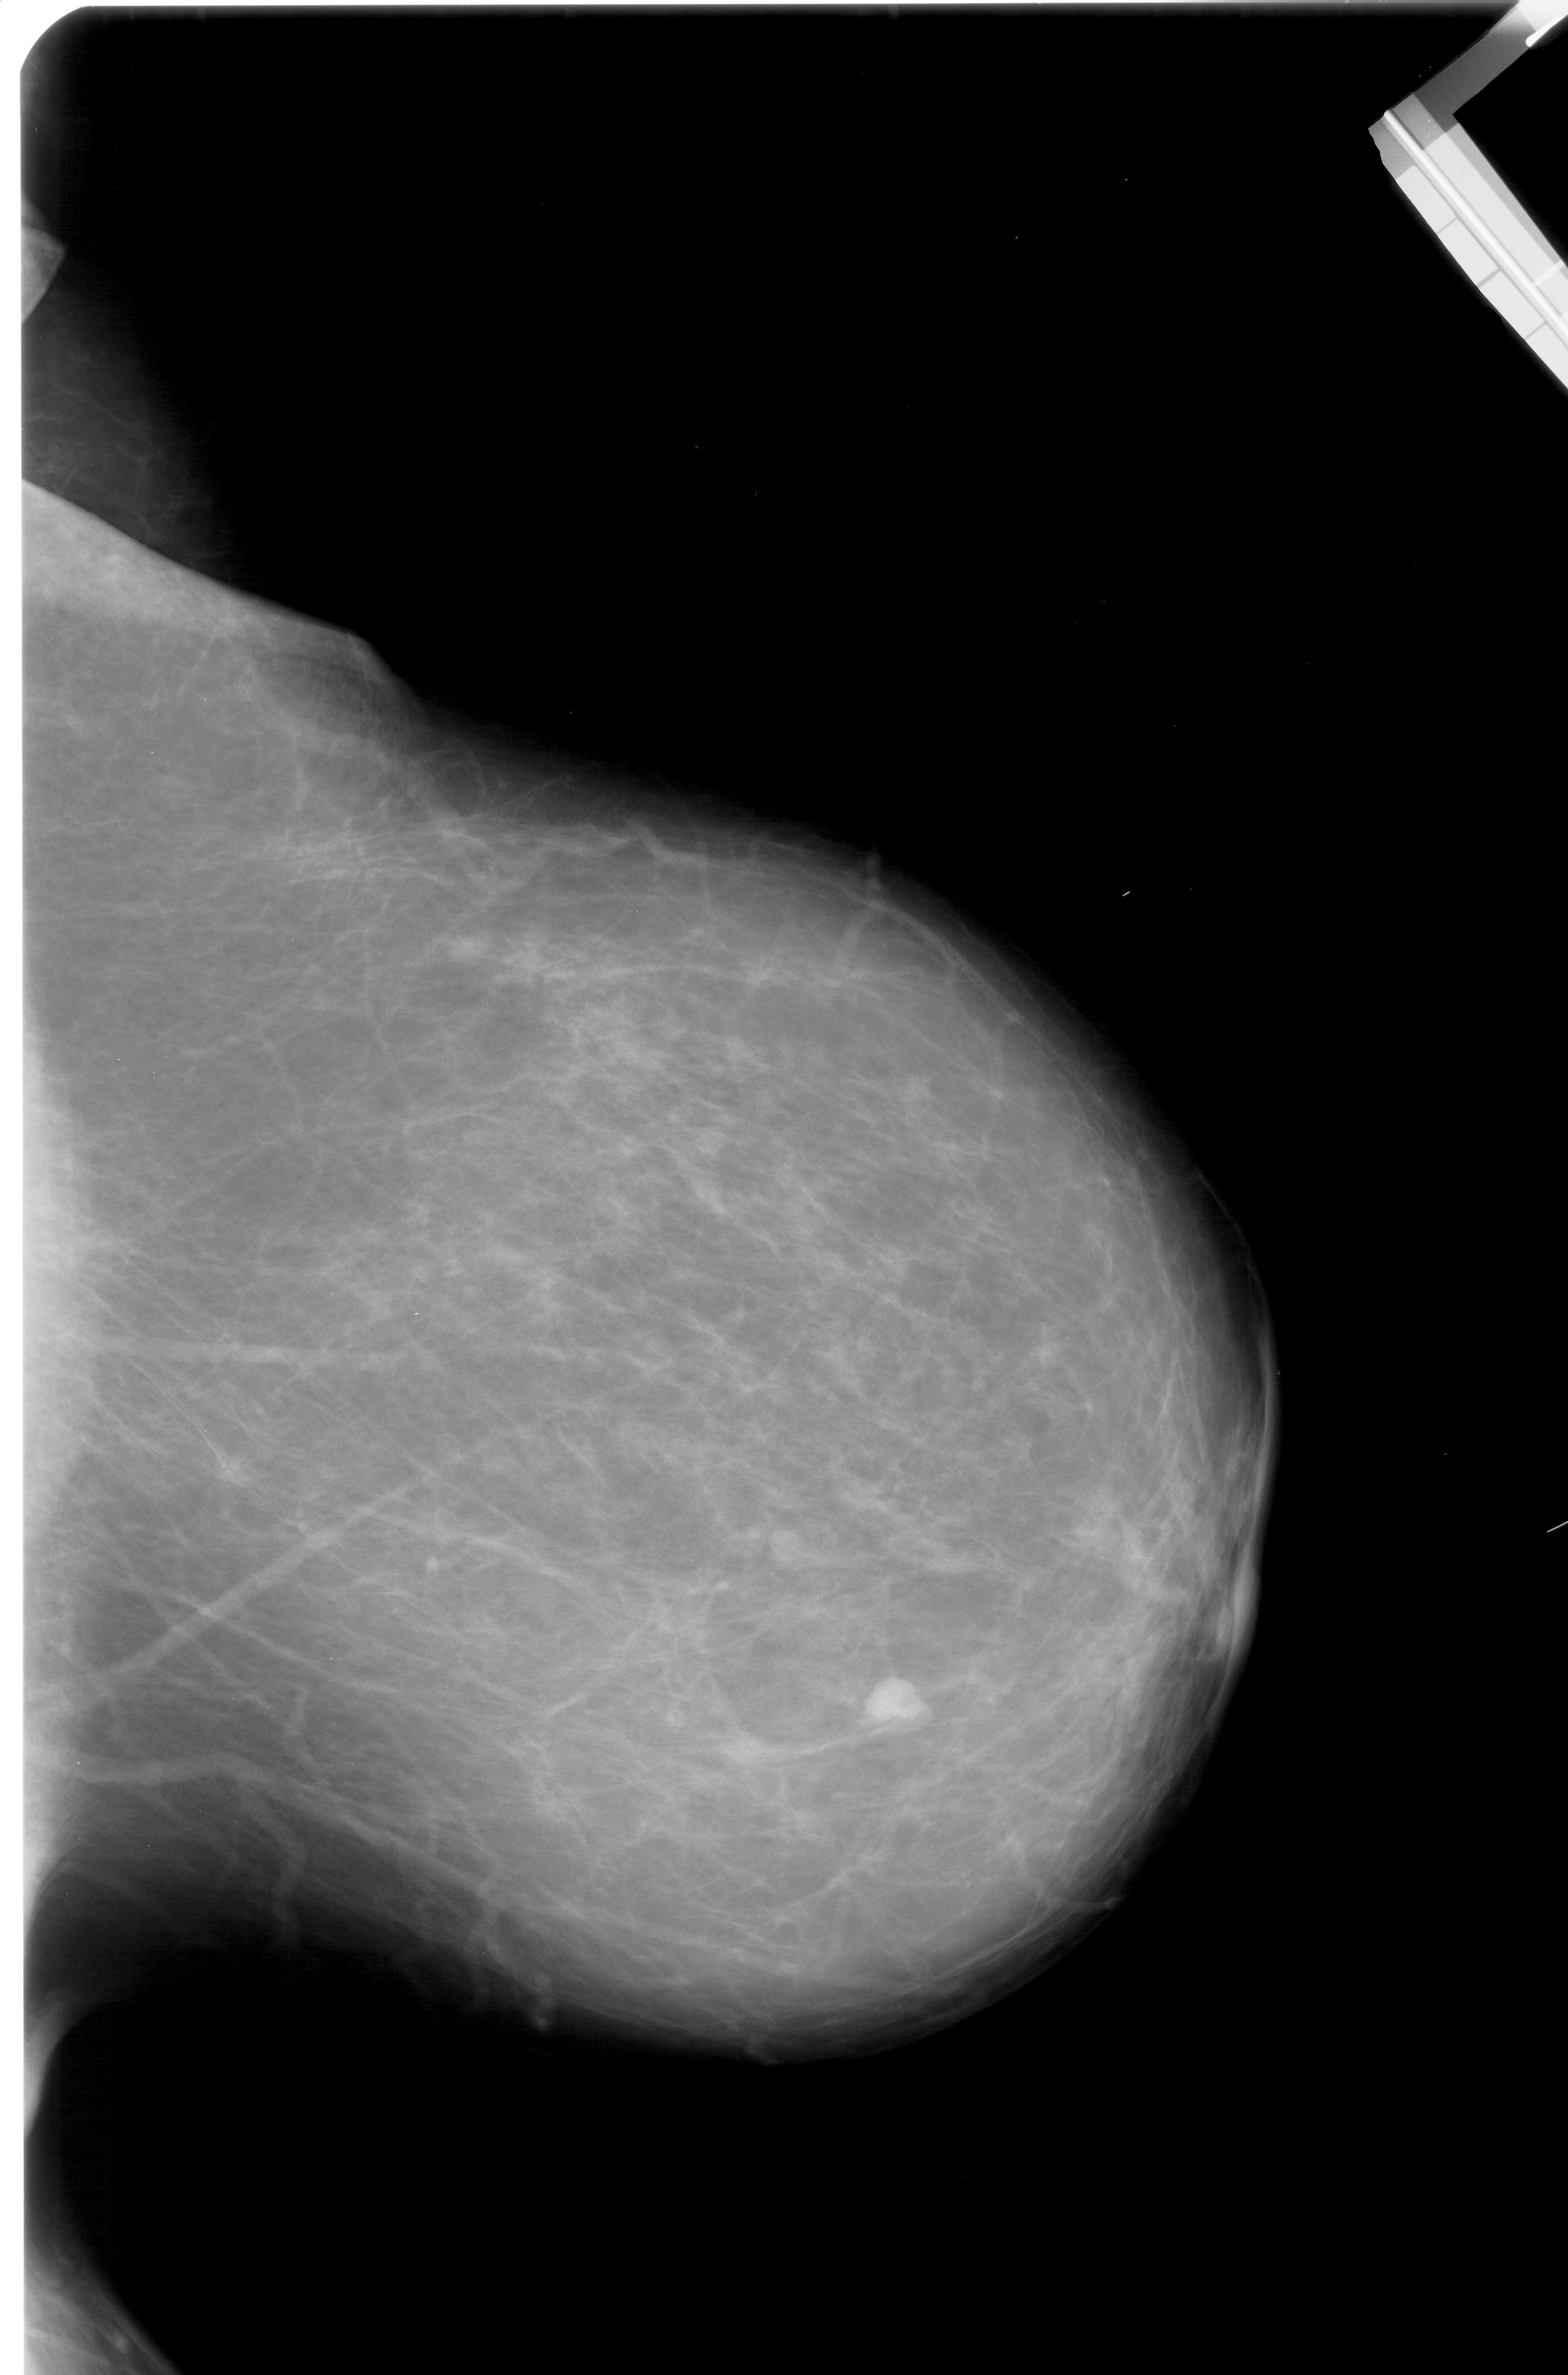
Mammogram (digitized film); right breast; CC view; breast composition: scattered fibroglandular densities (BI-RADS density category 2 of 4).
Abnormality record for this image: mass, shape lobulated, margins circumscribed; BI-RADS assessment category 4; subtlety rating 5 on a 1 (subtle) to 5 (obvious) scale; pathology (as recorded): malignant.